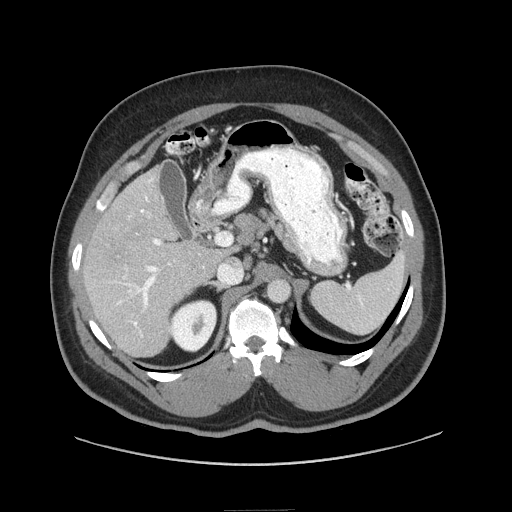
Contrast-enhanced abdominal CT (liver protocol), one axial slice; slice 45 of 87 in the series (ordered by position); reconstruction kernel STANDARD; 140 kVp; soft-tissue window (W 400 / L 40 HU); 2.5 mm slice thickness; 512 × 512 image matrix, field of view 440 × 440 mm. From the clinical record (not read from this slice): diagnosis: hepatocellular carcinoma (patient treated with transarterial chemoembolisation; whether this scan precedes or follows treatment is not stated here); TNM stage (as recorded): Stage-II; Child-Pugh class: A; tumour differentiation: moderately differentiated.
Annotated regions visible in this slice (semi-automatic segmentation, software-assisted and operator-edited):
- liver parenchyma outside the tumour (the mass and vessels are separate outlines, so this box may not span the whole liver): box from (x=82, y=166) to (x=224, y=356) px
- liver vessels: (x=113, y=178)–(x=204, y=338)